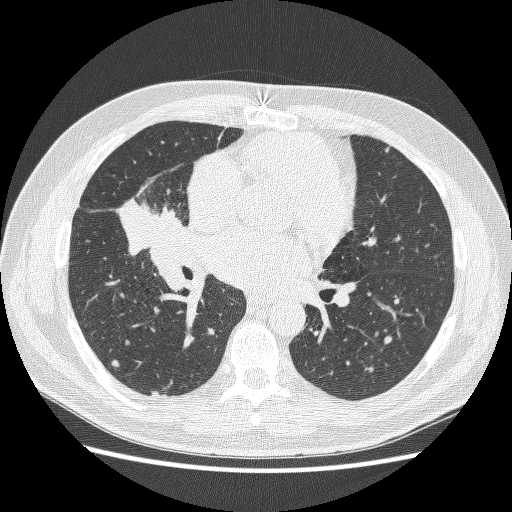
Axial slice from a low-dose chest CT screening exam, baseline screening round, lung window (W 1500 / L -600 HU), 1.25 mm slice thickness, lung (sharp) reconstruction kernel (BONE), slice 135 of 251 in the series. Male, age 59 years at enrolment. Former smoker at enrolment.
Lesion marked by an expert reader, bounding box [x1, y1, x2, y2] px = [119, 182, 197, 258]. No non-calcified nodule or mass ≥4 mm was recorded by the screening reader at this exam. Official screen result: positive, change unspecified: nodule(s) >= 4 mm or enlarging nodule(s), mass(es), or other non-specific abnormalities suspicious for lung cancer. Lung cancer was diagnosed 24 days after this screen: adenocarcinoma, NOS, right middle lobe, poorly differentiated (G3), stage IV (AJCC 6th edition), 54 mm at pathology.